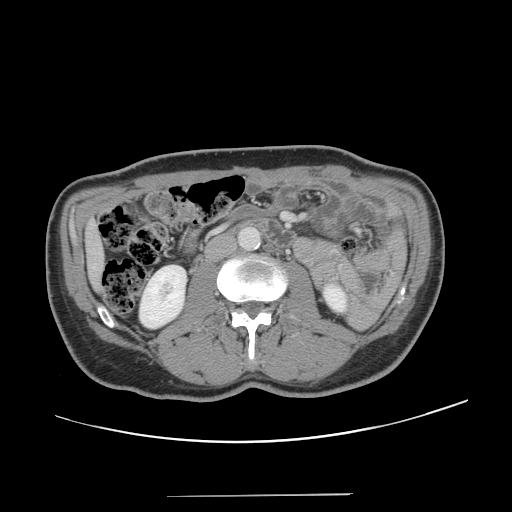
Contrast-enhanced abdominal CT, one axial slice; position 41 of 131 along the scan axis; soft-tissue window (W 400 / L 40 HU); 512 × 512 image matrix. Male patient, age 60 years. From the clinical record (not read from this slice): diagnosis: colorectal cancer liver metastases, imaged before liver resection; multiple liver metastases: no; largest metastasis: 2.5 cm; chemotherapy before resection: no.
Structures marked on this image (expert manual segmentation):
- liver: box from (x=88, y=227) to (x=102, y=286) px
- planned liver remnant (the part of the liver to remain after resection): (x=88, y=226)–(x=102, y=286)